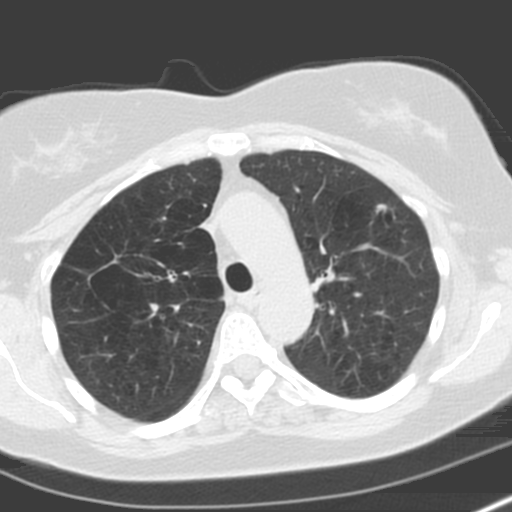
Chest CT (low-dose screening protocol), one axial image, baseline screening round, lung window (W 1500 / L -600 HU), 3.2 mm slice thickness, slice 52 of 173 in the series, 512 × 512 image matrix. Female participant, aged 57 years at enrolment. Former smoker at enrolment.
Expert-annotated lung lesion, box from (x=360, y=200) to (x=399, y=231) px. Screening reader's record for this exam: no non-calcified nodule ≥4 mm recorded. Official screen result: negative screen, minor abnormalities not suspicious for lung cancer. Participant outcome: lung cancer diagnosed 503 days after this screen (after the second annual screen) — adenocarcinoma, NOS, left upper lobe, moderately differentiated (G2), stage IA (AJCC 6th edition), 18 mm at pathology.